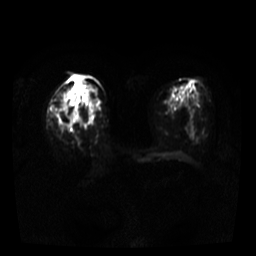
Breast MRI, one axial slice. Position 15 of 37 along the scan axis. Diffusion-weighted series; image 2 of 4 stored at this slice position (different b-values; order by instance number). 3 T. 256 × 256 image matrix, field of view 320 × 320 mm. Female patient.
Structures marked on this image (expert manual segmentation):
- tumour on diffusion-weighted imaging: box from (x=62, y=118) to (x=73, y=130) px